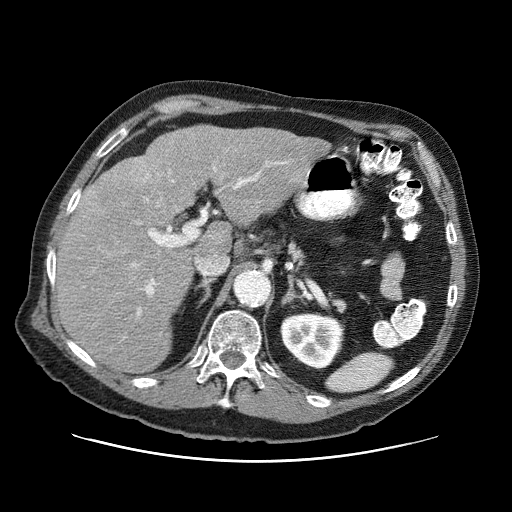
Contrast-enhanced abdominal CT (liver protocol), one axial slice; position 44 of 87 along the scan axis; one of 3 acquisitions stored at this slice position; soft-tissue window (W 400 / L 40 HU); 2.5 mm slice thickness; 512 × 512 image matrix. Case-level facts recorded for this patient, not image findings: diagnosis: hepatocellular carcinoma (patient treated with transarterial chemoembolisation; whether this scan precedes or follows treatment is not stated here); TNM stage (as recorded): Stage-IIIA; Child-Pugh class: A; tumour nodularity: multinodular.
Outlined on this slice (semi-automatically segmented with operator editing):
- liver parenchyma outside the tumour (the mass and vessels are separate outlines, so this box may not span the whole liver): box from (x=56, y=126) to (x=330, y=372) px
- liver vessels: (x=132, y=161)–(x=286, y=315)